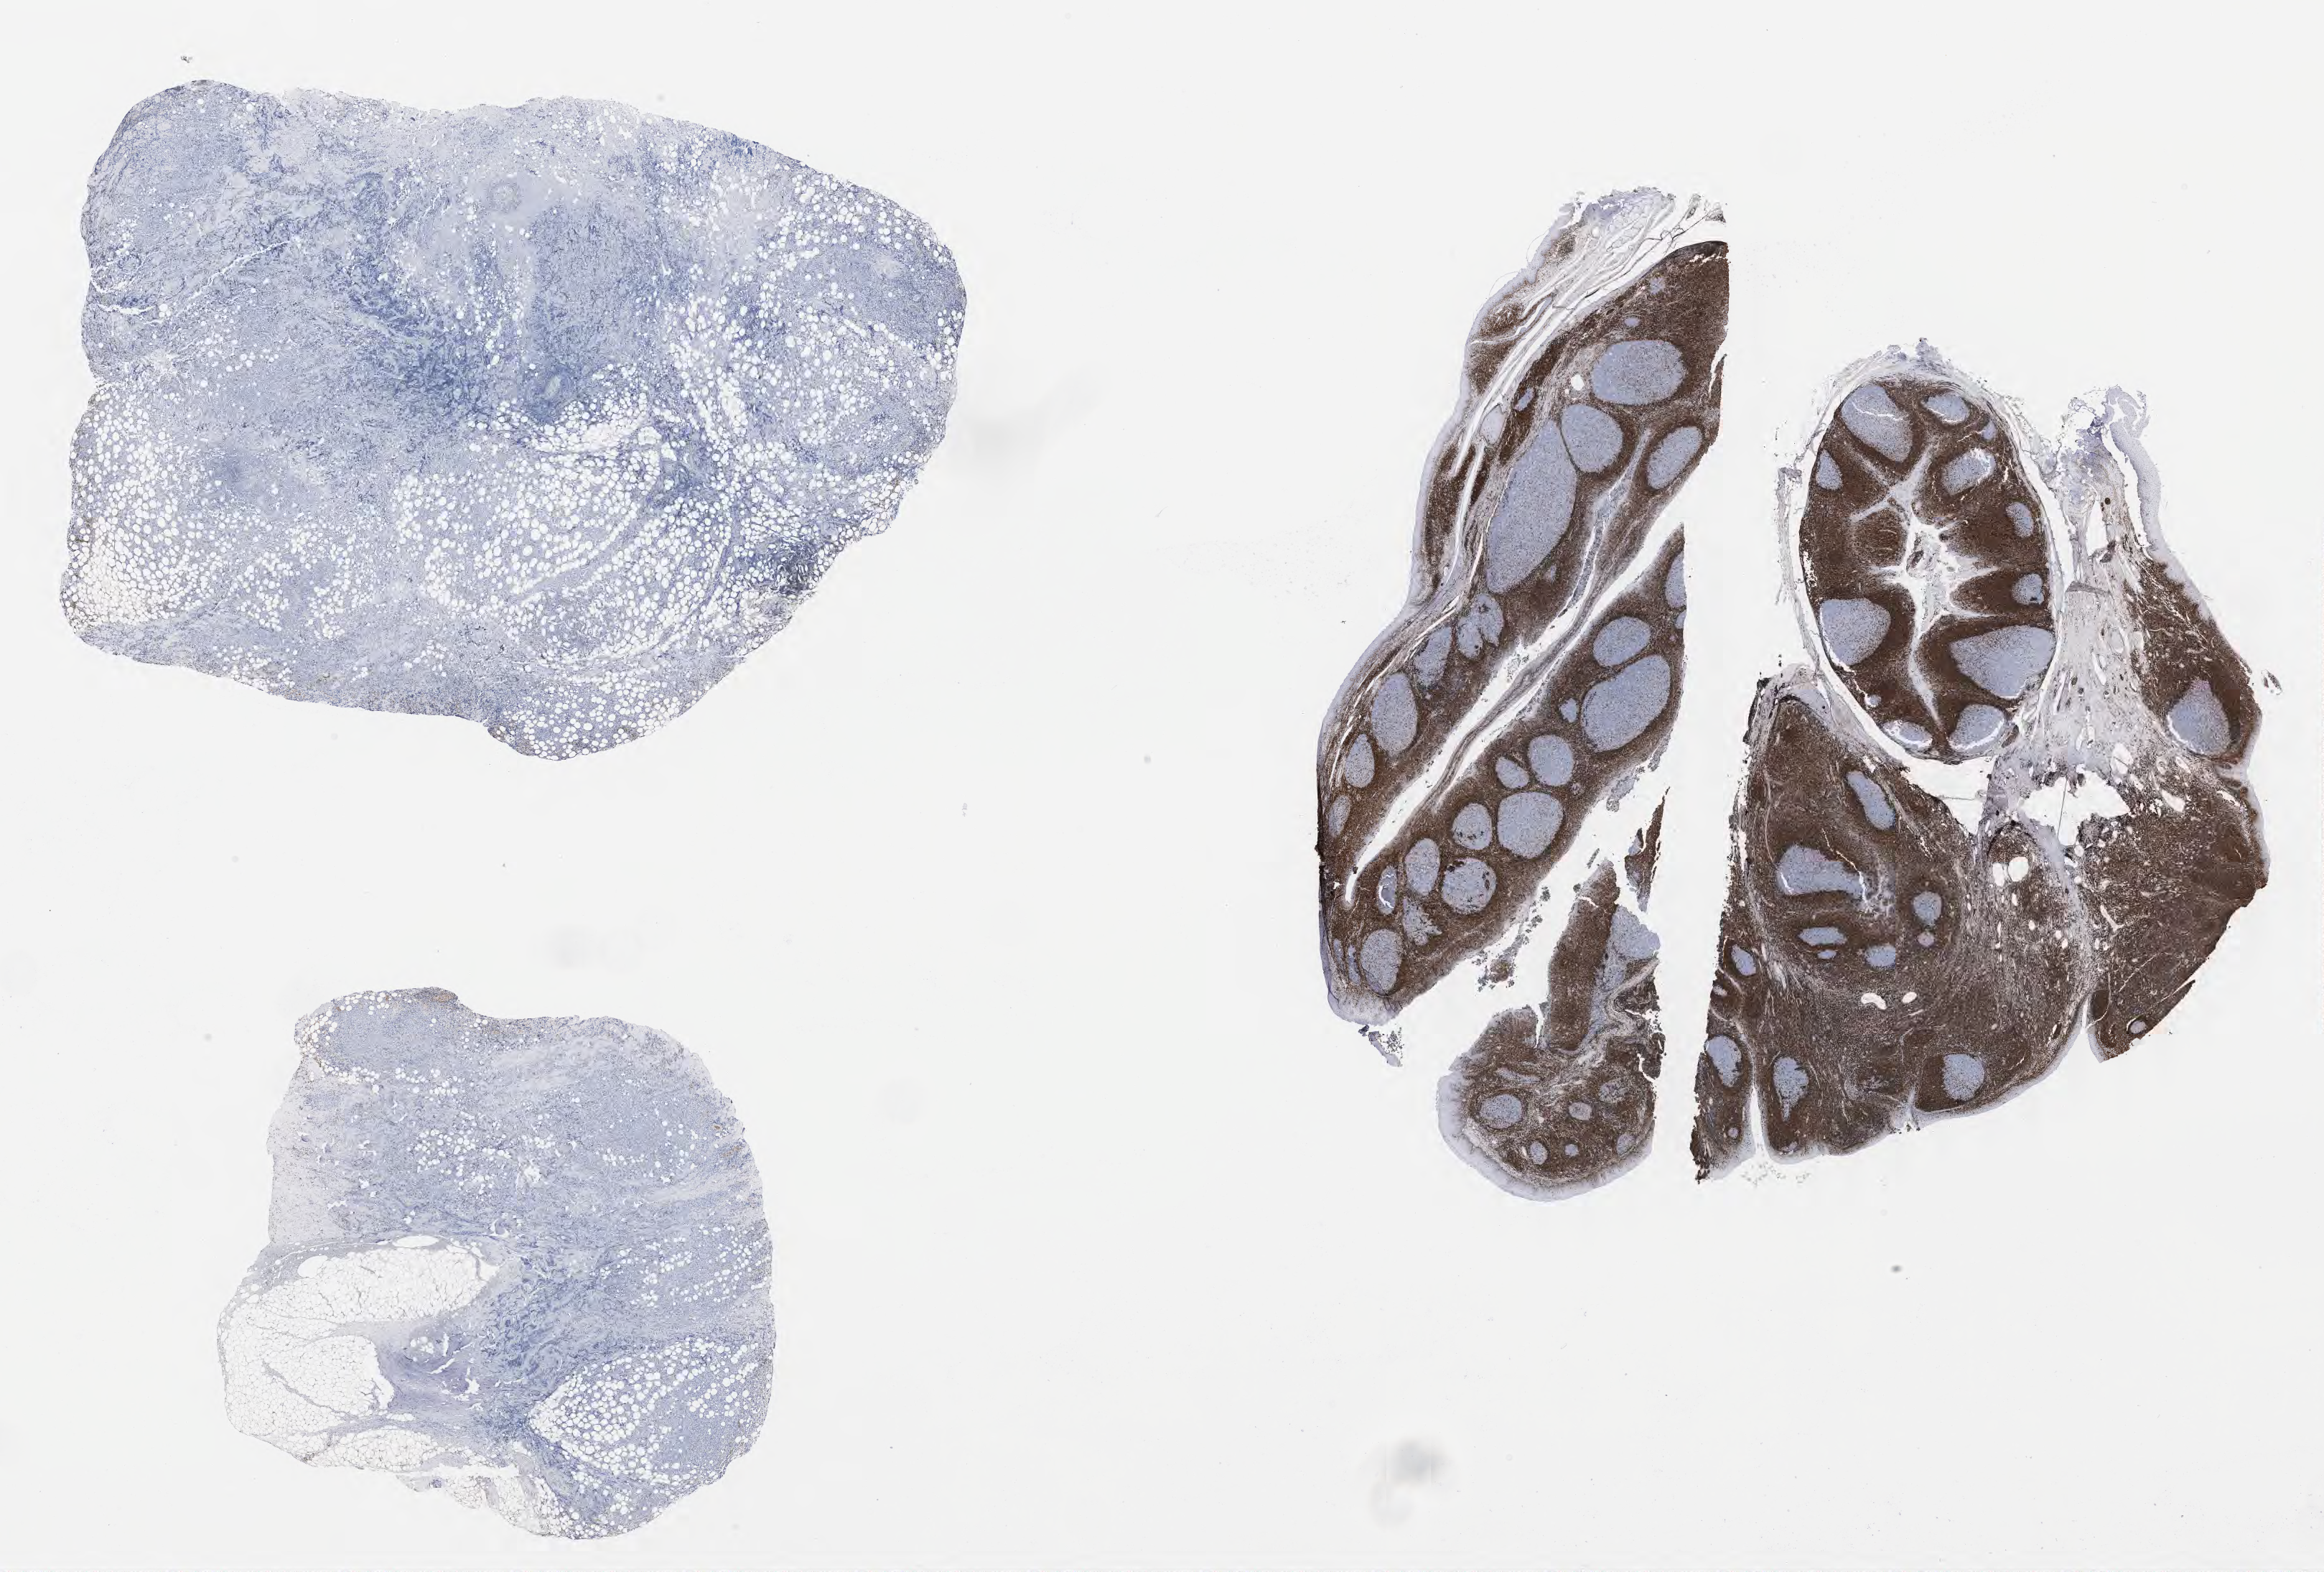
Whole-slide image, immunohistochemical stain for BCL2, low-resolution overview of the scanned area, about 26.2 x 17.7 mm, tumor tissue, site: kidney. Patient male; 63 years old.
Histologic diagnosis: Diffuse large B-cell lymphoma, NOS.